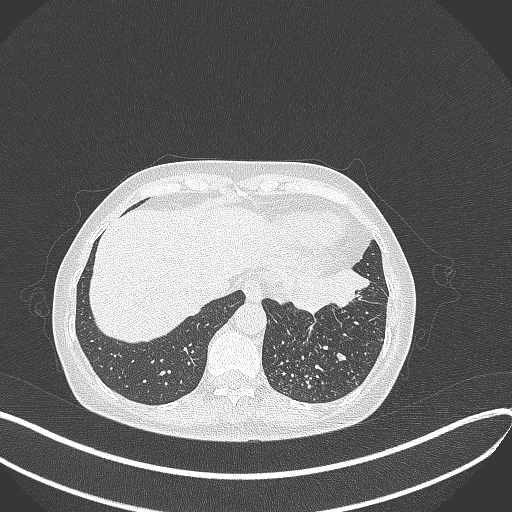
Chest CT, one axial slice. Position 87 of 429 along the scan axis. 100 kVp. Lung window (W 1500 / L -600 HU). 1 mm slice thickness. 512 × 512 image matrix, field of view 400 × 400 mm. Female patient, age 63 years. Case-level facts recorded for this patient, not image findings: clinical TNM (as recorded): T1b N0 M0; histopathological grade: G2-3.
Annotated regions visible in this slice (bounding box drawn by a radiologist):
- lung tumour (recorded histology: adenocarcinoma): bounding box [x1, y1, x2, y2] px = [276, 267, 370, 314]